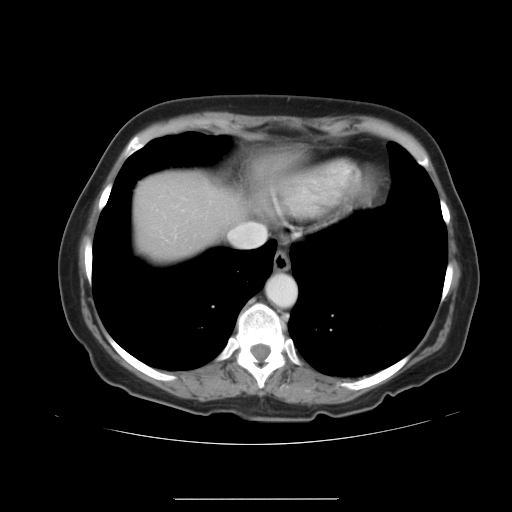
Contrast-enhanced abdominal CT, one axial slice. Slice 35 of 41 in the series (ordered by position). 120 kVp. Intravenous contrast given. Soft-tissue window (W 400 / L 40 HU). 5 mm slice thickness. 512 × 512 image matrix. Female patient, age 63 years. Case-level facts recorded for this patient, not image findings: diagnosis: colorectal cancer liver metastases, imaged before liver resection; multiple liver metastases: yes; largest metastasis: 1.5 cm; disease in both lobes: yes.
Structures marked on this image (manually delineated by an expert):
- liver: bounding box (x1, y1, x2, y2) in pixels: (132, 172, 242, 263)
- planned liver remnant (the part of the liver to remain after resection): (132, 172, 240, 263)